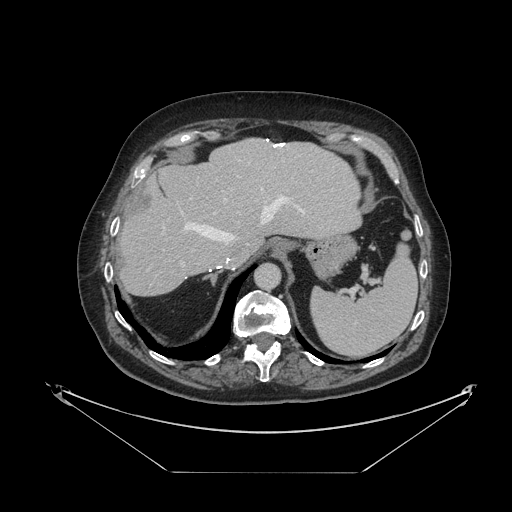
Contrast-enhanced abdominal CT, one axial slice. Position 83 of 121 along the scan axis. Reconstruction kernel STANDARD. Soft-tissue window (W 400 / L 40 HU). 512 × 512 image matrix. Male patient, age 68 years. From the clinical record (not read from this slice): diagnosis: colorectal cancer liver metastases, imaged before liver resection.
Outlined on this slice (manually delineated by an expert):
- hepatic veins: bounding box (x1, y1, x2, y2) in pixels: (182, 163, 306, 241)
- liver: (120, 139, 360, 295)
- planned liver remnant (the part of the liver to remain after resection): (120, 139, 360, 295)
- portal vein (with intrahepatic branches): (181, 198, 227, 266)
- liver metastasis: (134, 192, 153, 212)